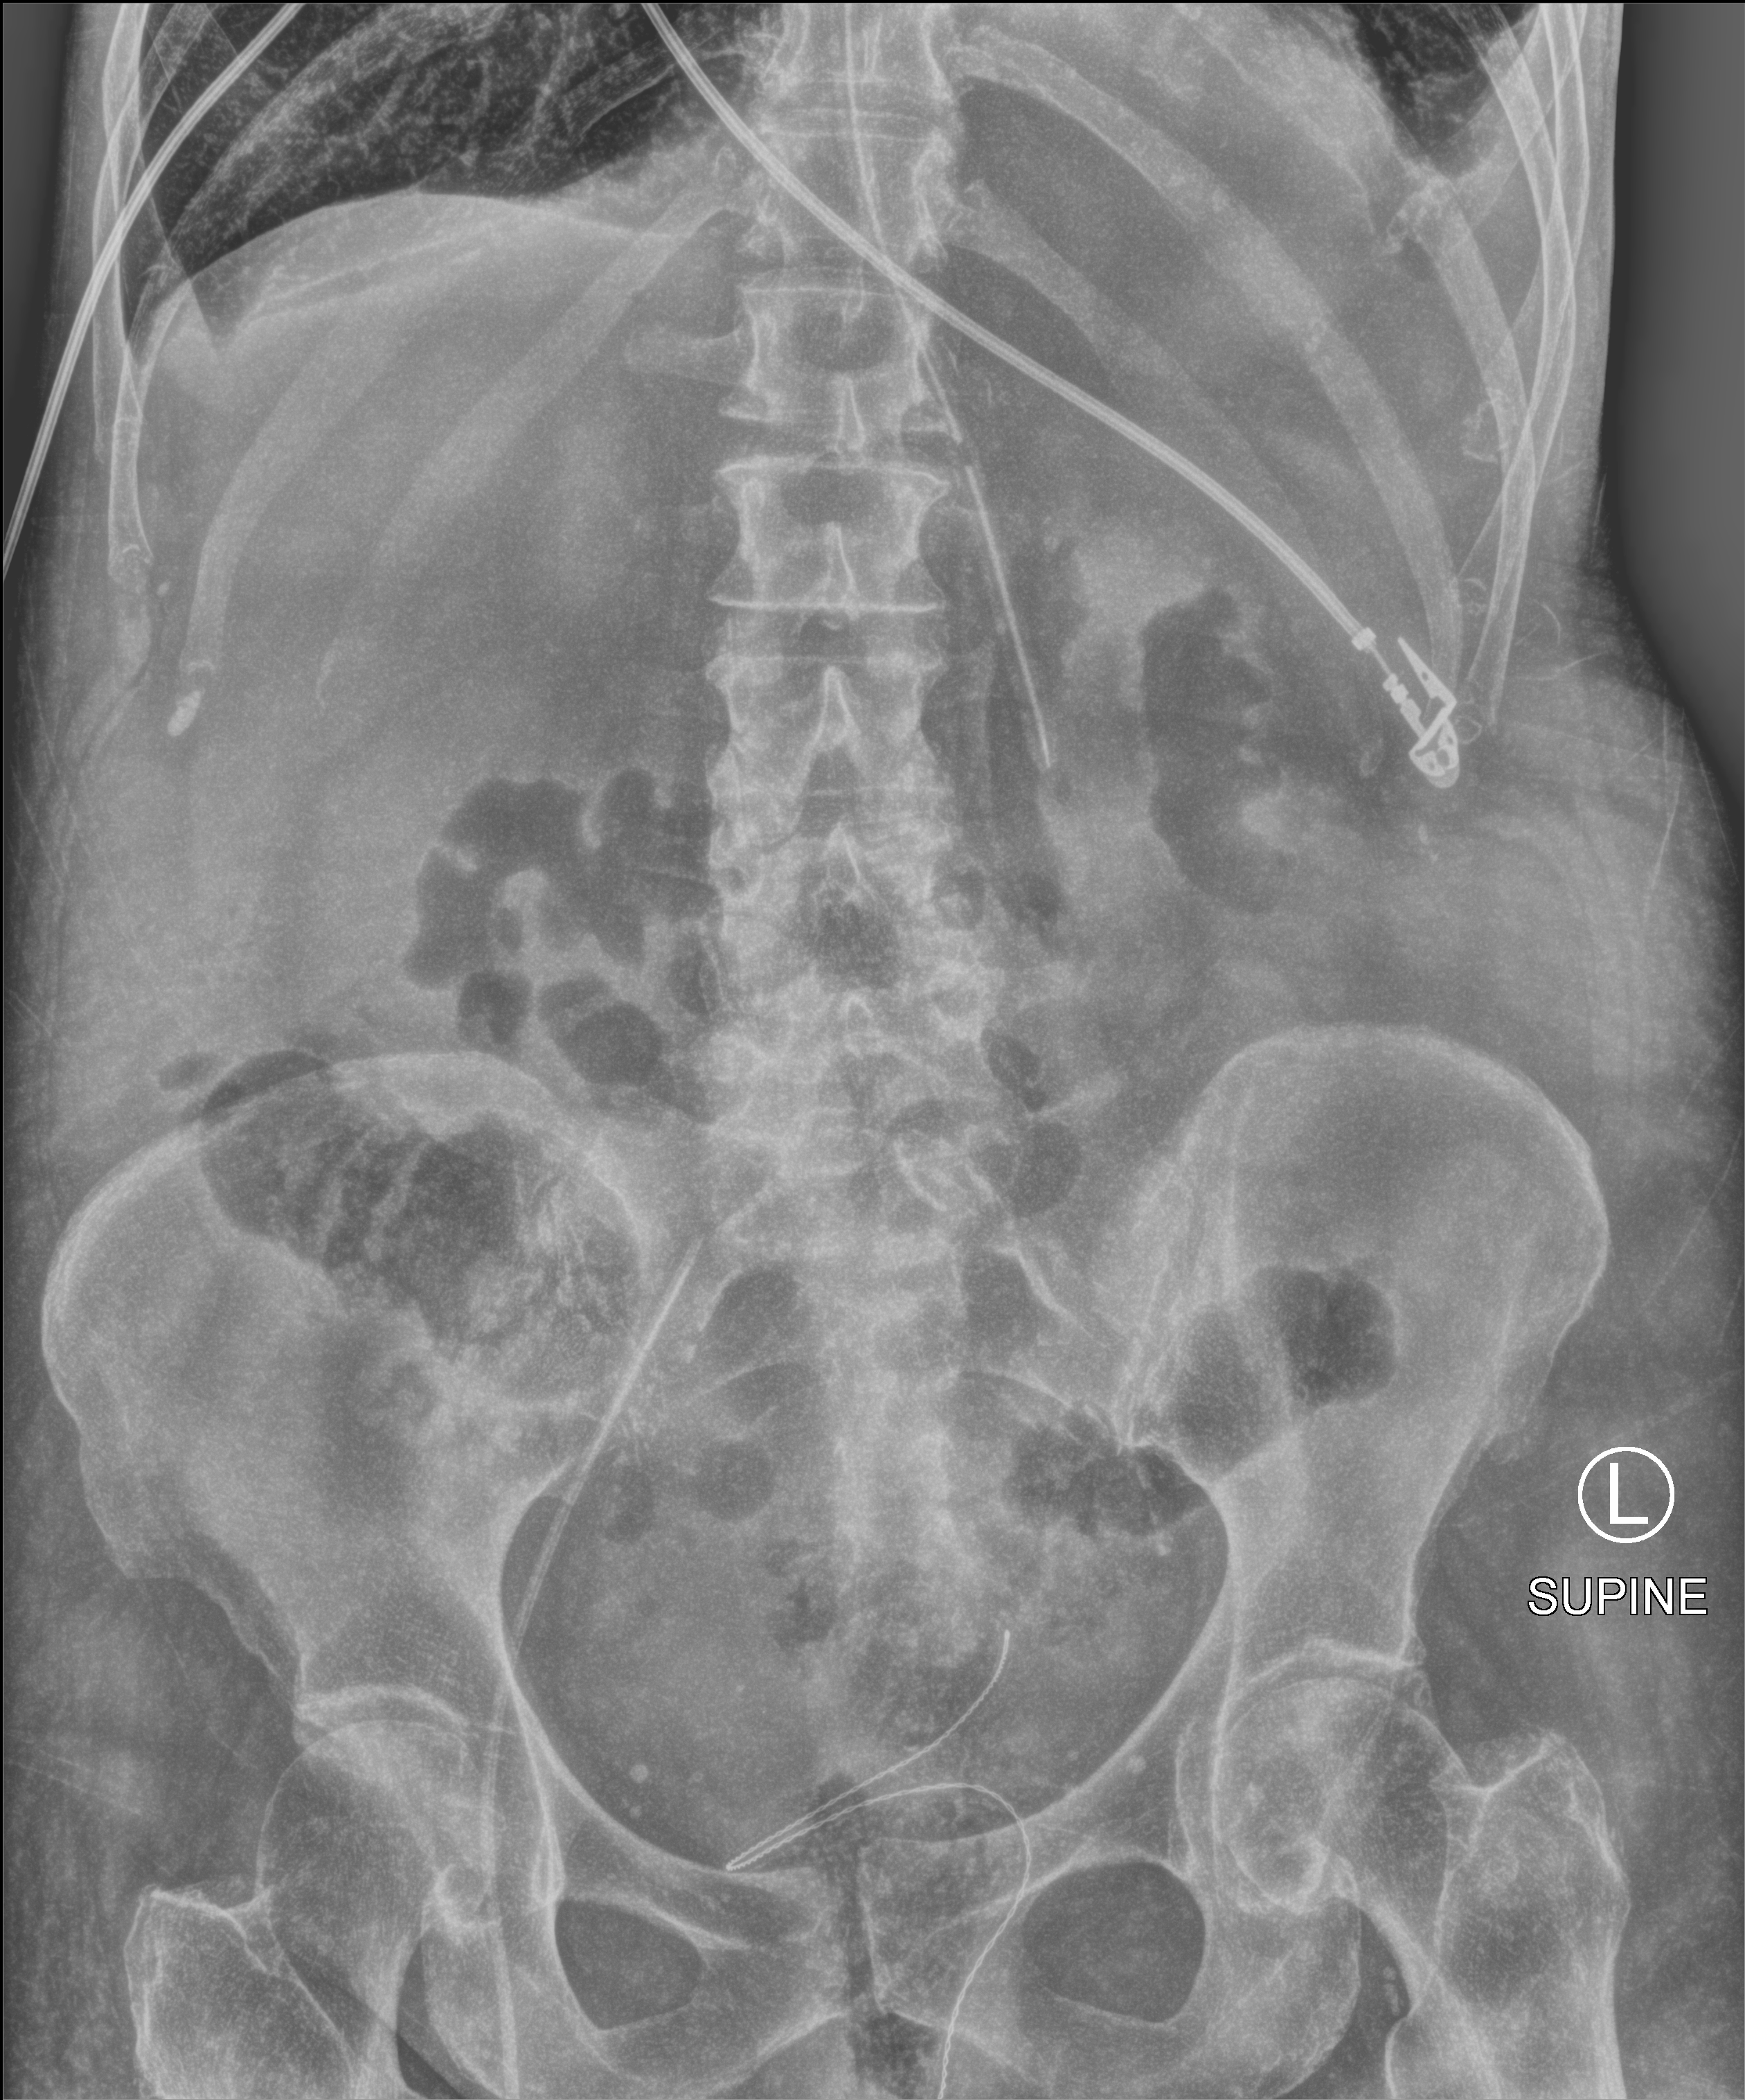
Portable abdomen radiograph; anteroposterior (AP) projection. Patient hospitalised with COVID-19; female, aged 60–74 years.
Hospital-stay facts (about this admission, not read from this image; timing relative to this image not recorded):
- mechanically ventilated during this hospital stay: yes
- admitted to intensive care during this hospital stay: yes
- length of hospital stay: 38 days